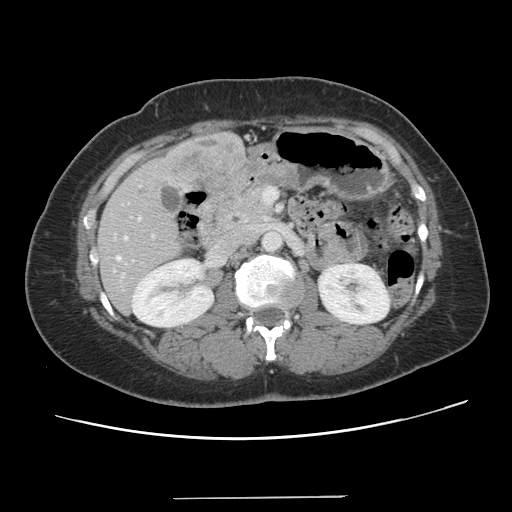
Contrast-enhanced abdominal CT, one axial slice. Position 55 of 141 along the scan axis. Intravenous contrast given. Soft-tissue window (W 400 / L 40 HU). 2.5 mm slice thickness. 512 × 512 image matrix. Female patient, age 53 years. Case-level facts recorded for this patient, not image findings: diagnosis: colorectal cancer liver metastases, imaged before liver resection; multiple liver metastases: no; largest metastasis: 14.5 cm; disease in both lobes: yes.
Structures marked on this image (outlined manually by an expert reader):
- hepatic veins: box from (x=116, y=236) to (x=126, y=260) px
- liver: (x=97, y=132)–(x=245, y=313)
- planned liver remnant (the part of the liver to remain after resection): (x=97, y=217)–(x=182, y=313)
- portal vein (with intrahepatic branches): (x=138, y=217)–(x=153, y=236)
- liver metastasis: (x=174, y=135)–(x=242, y=187)